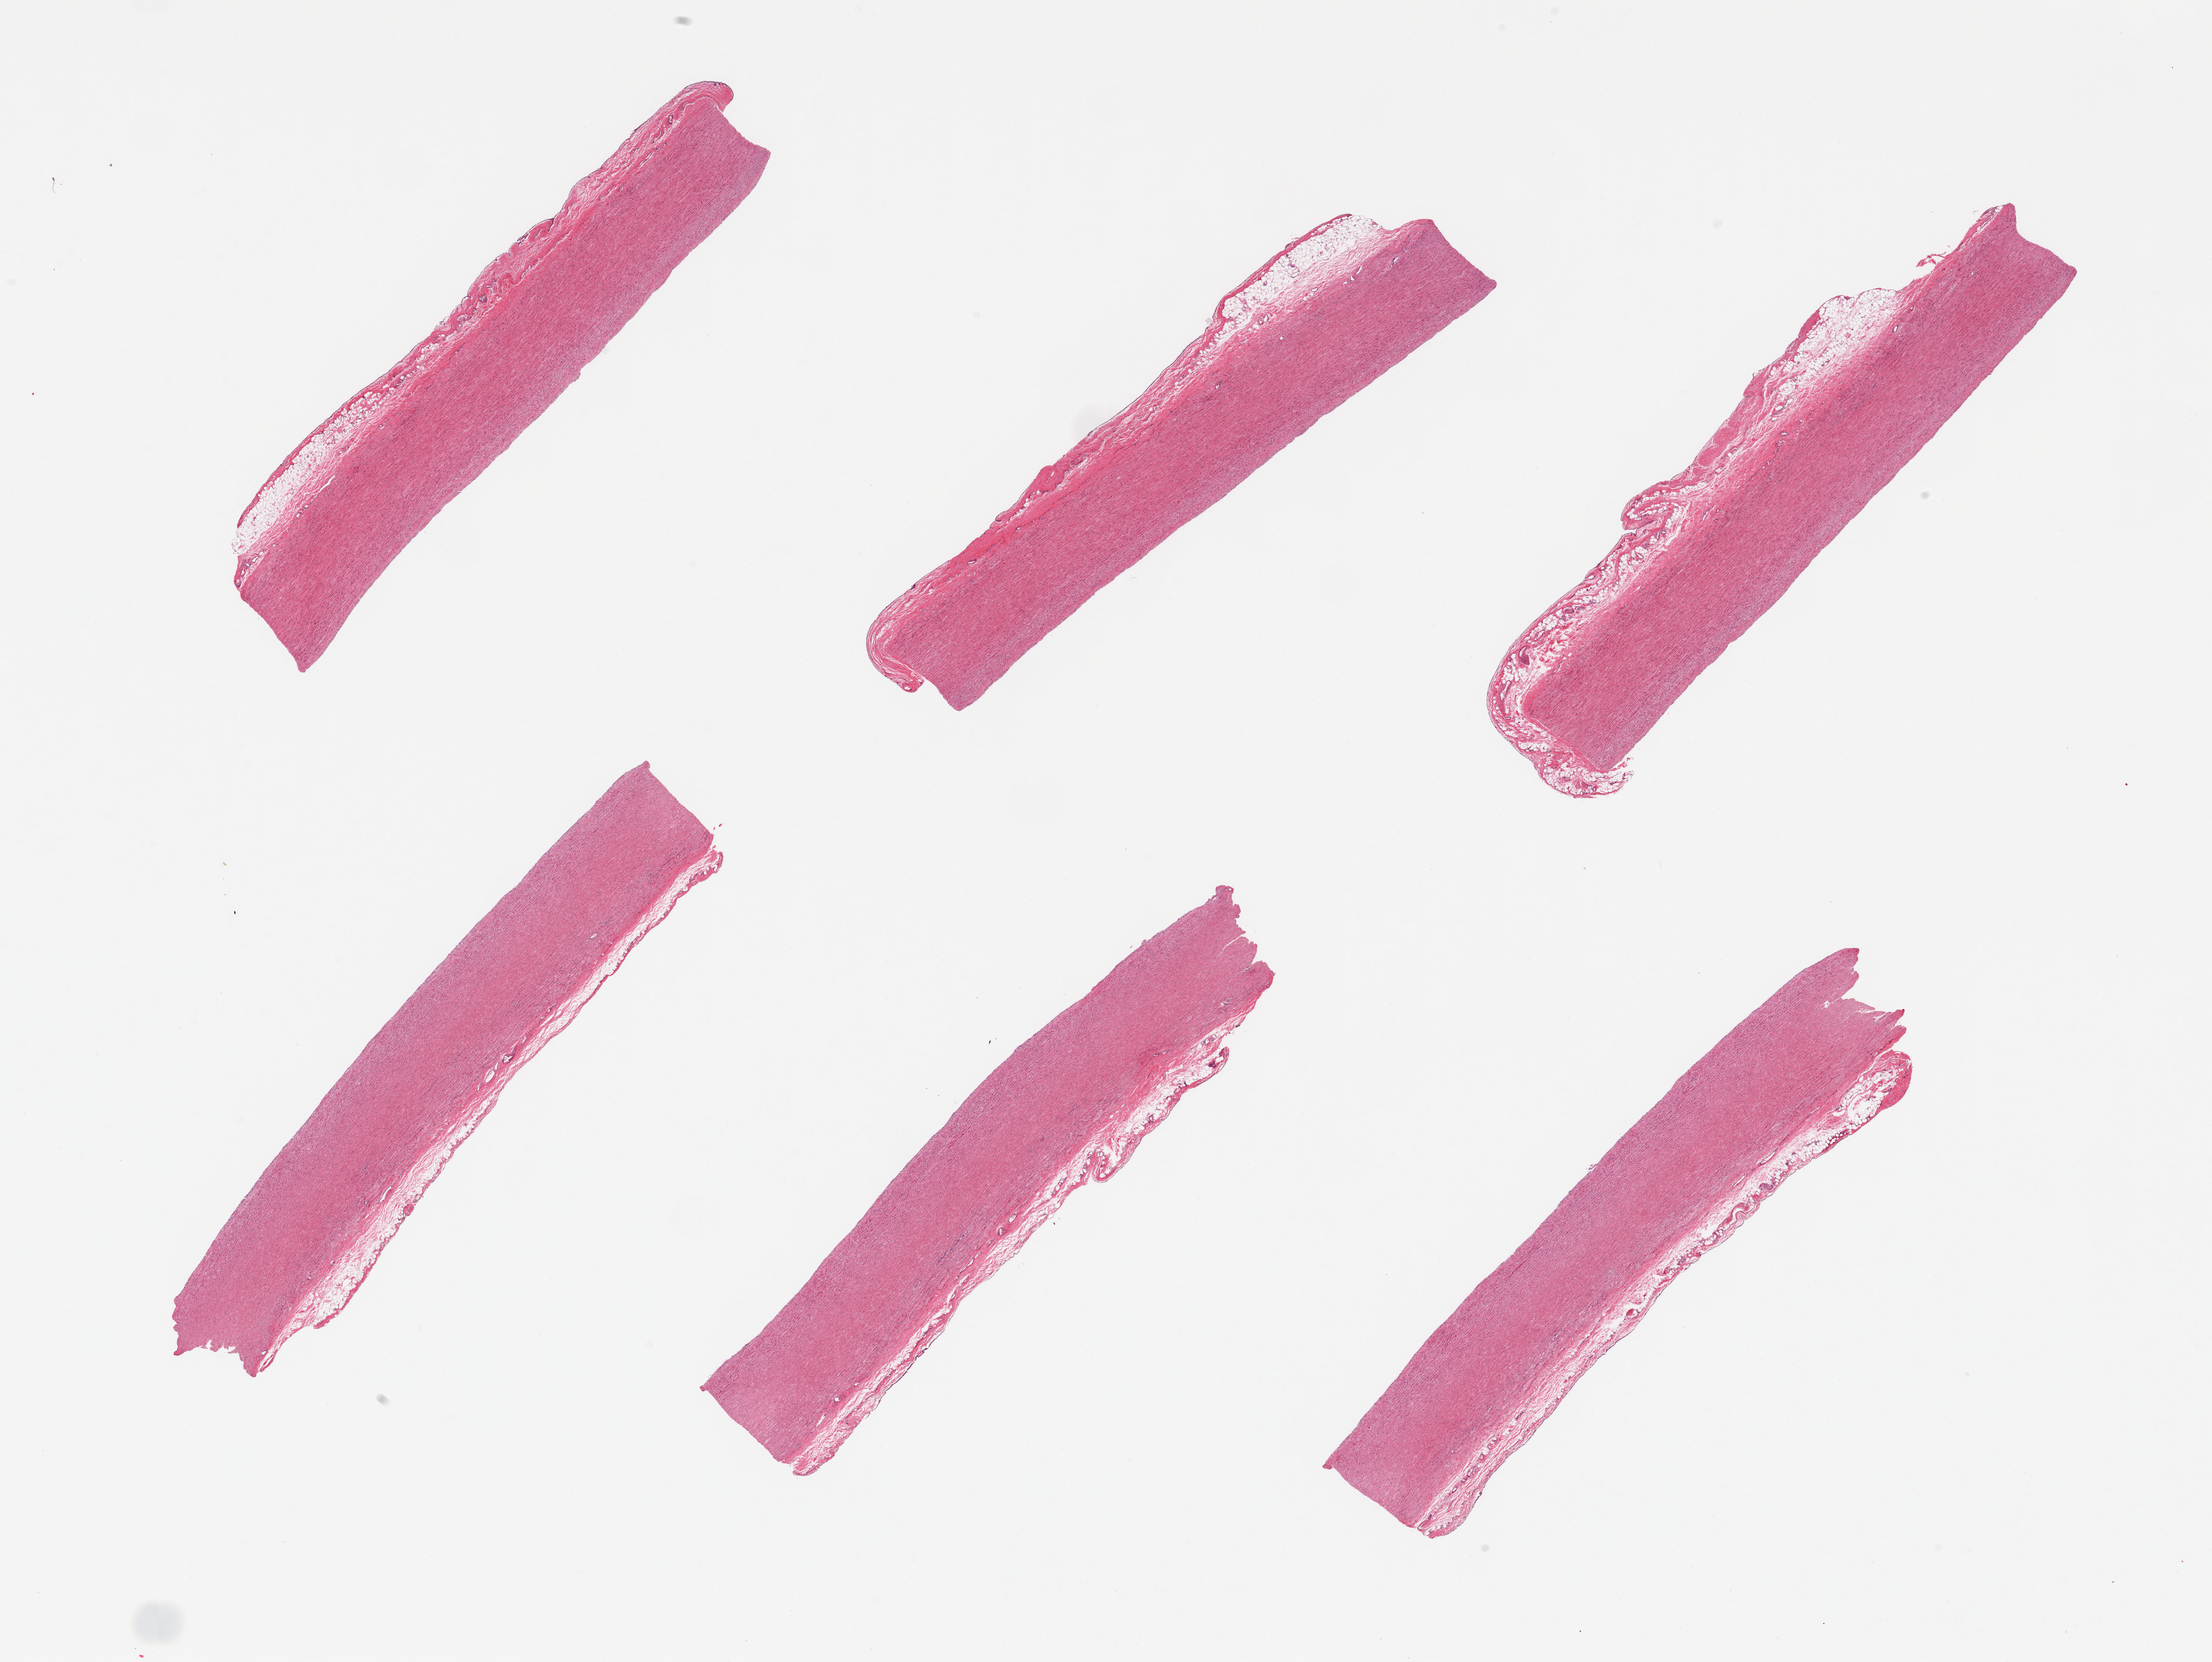
Haematoxylin and eosin whole-slide image, brightfield — low-resolution overview of the scanned area, about 27.6 x 20.7 mm, PAXgene-fixed, paraffin-embedded tissue, section of aorta (target tissue), donor tissue sample. Donor: male.
Reviewer comment on this tissue sample: 6 pieces; up to 0.8mm rim of adherent adventitia.